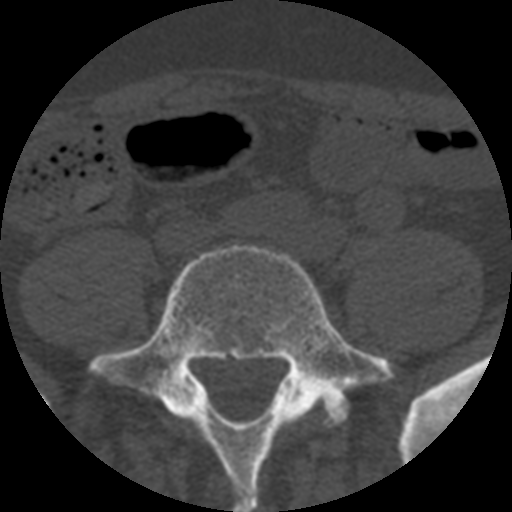
CT including the spine, one axial slice. Slice 66 of 508 in the series (ordered by position). Reconstruction kernel STANDARD. 120 kVp. Bone window (W 1800 / L 400 HU). 1.25 mm slice thickness. 512 × 512 image matrix. Patient age 57 years. Case-level facts recorded for this patient, not image findings: primary cancer: prostate.
Outlined on this slice (semi-automatically segmented with operator editing):
- L5 vertebra: bounding box [x1, y1, x2, y2] px = [88, 244, 395, 512]